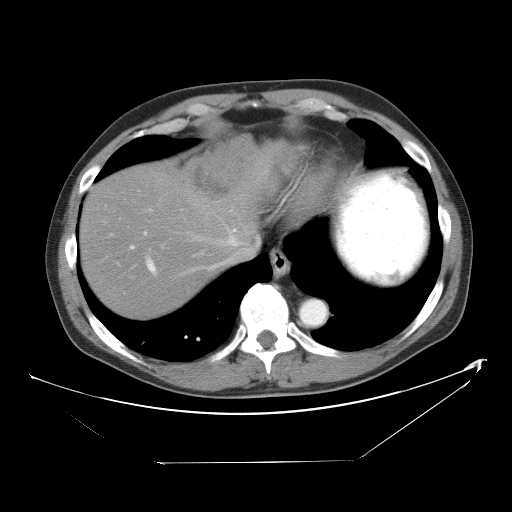
Contrast-enhanced abdominal CT, one axial slice; slice 45 of 53 in the series (ordered by position); intravenous contrast given; soft-tissue window (W 400 / L 40 HU); 5 mm slice thickness; 512 × 512 image matrix, field of view 438 × 438 mm. Male patient, age 59 years. Case-level facts recorded for this patient, not image findings: diagnosis: colorectal cancer liver metastases, imaged before liver resection; multiple liver metastases: yes; largest metastasis: 8.5 cm; disease in both lobes: no.
Structures marked on this image (outlined manually by an expert reader):
- hepatic veins: bounding box (x1, y1, x2, y2) in pixels: (209, 232, 259, 269)
- liver: (81, 141, 289, 317)
- planned liver remnant (the part of the liver to remain after resection): (81, 172, 227, 317)
- portal vein (with intrahepatic branches): (144, 210, 236, 273)
- liver metastasis: (191, 143, 248, 197)